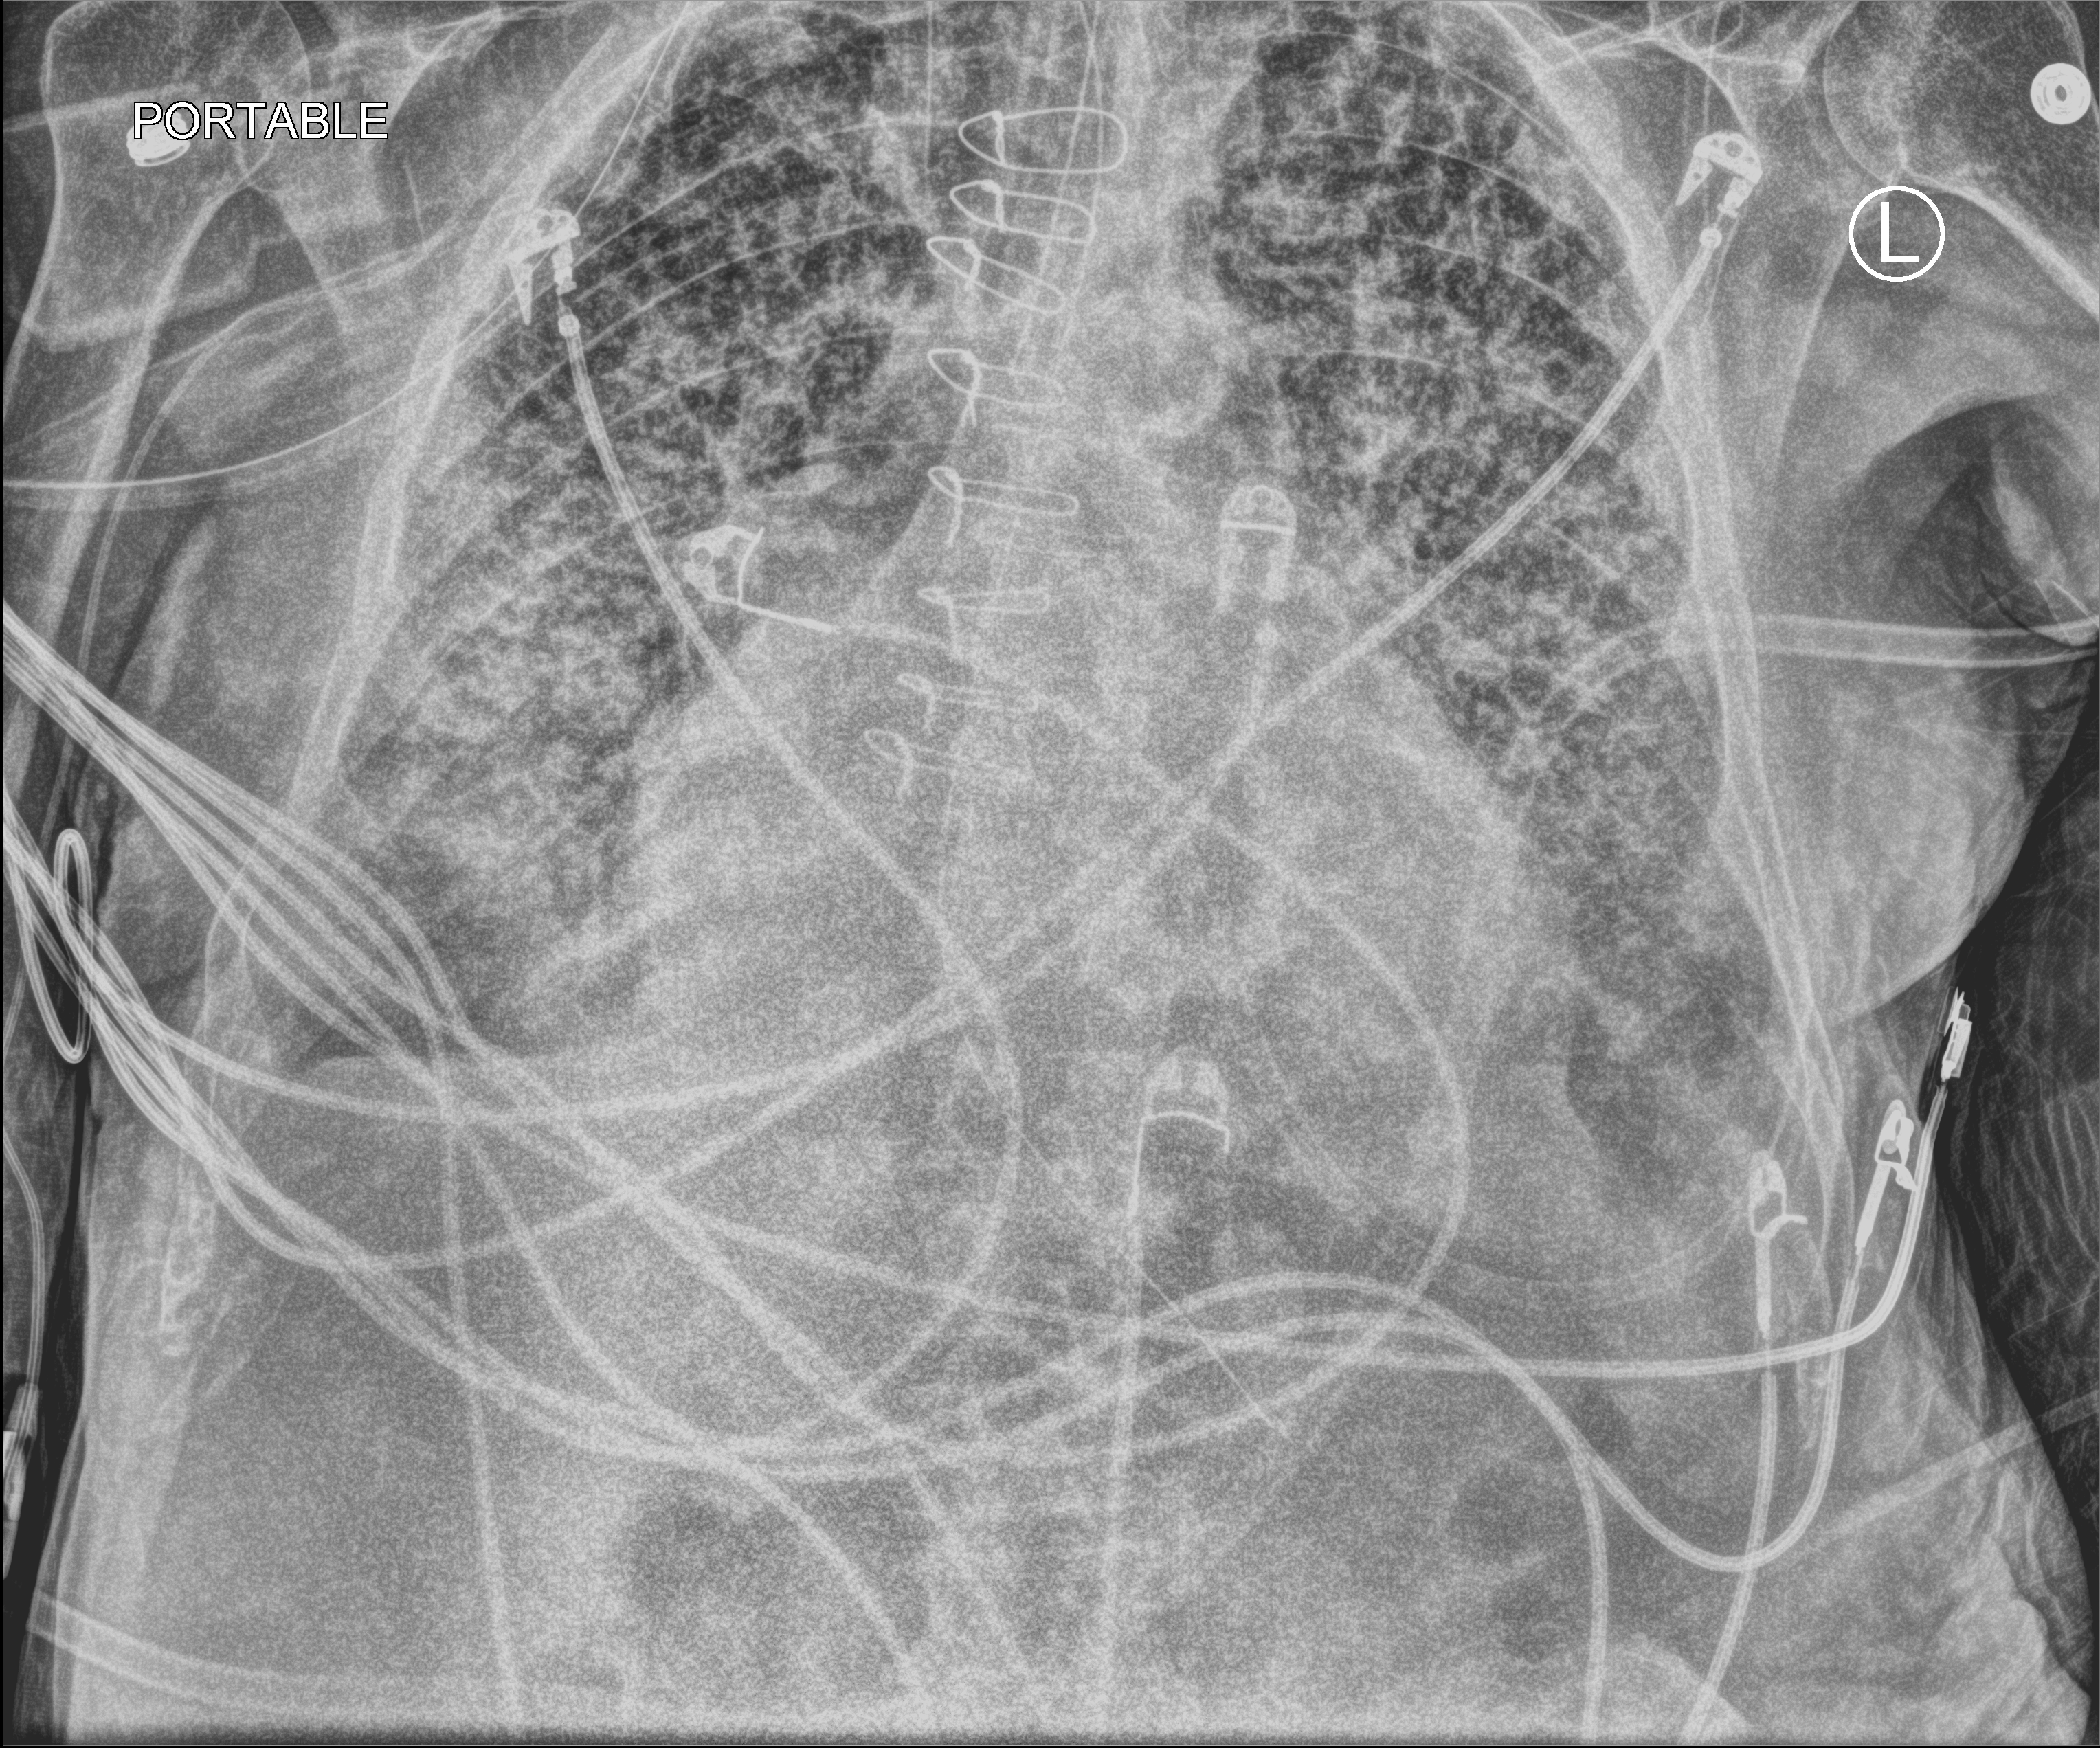
Portable chest radiograph; anteroposterior (AP) projection. Patient hospitalised with COVID-19; male, aged 75–90 years.
Admission-level facts for this patient (not findings on this image; timing relative to this image not recorded):
- mechanically ventilated during this hospital stay: yes
- admitted to intensive care during this hospital stay: yes